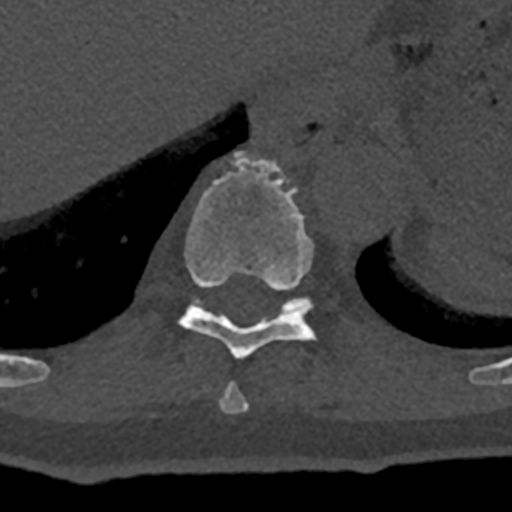
CT including the spine, one axial slice; slice 597 of 797 in the series (ordered by position); reconstruction kernel Br40s/3; 120 kVp; bone window (W 1800 / L 400 HU); 512 × 512 image matrix, field of view 160 × 160 mm. Patient: male, 74 years. Case-level facts recorded for this patient, not image findings: primary cancer: renal; vertebrae with lytic lesions (as recorded): T10, L1, L2, L3, L4, L5.
Outlined on this slice (semi-automatic segmentation, software-assisted and operator-edited):
- T10 vertebra: bounding box <179,151,315,359> (left, top, right, bottom; pixels)
- T11 vertebra: <195,297,313,313>
- T9 vertebra: <220,383,249,413>